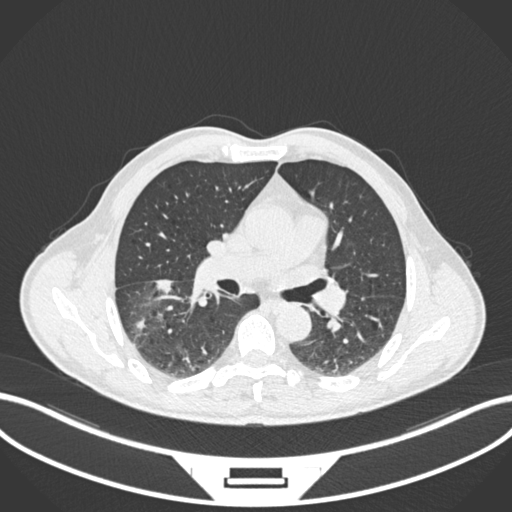
Chest CT, one axial slice; position 111 of 208 along the scan axis; 120 kVp; lung window (W 1500 / L -600 HU); 1 mm slice thickness; 512 × 512 image matrix, field of view 400 × 400 mm. Patient: male, 58 years. From the clinical record (not read from this slice): clinical TNM (as recorded): T3 N0 M0.
Outlined on this slice (rectangle marked by the reading radiologist):
- lung tumour (recorded histology: squamous cell carcinoma): bounding box [x1, y1, x2, y2] px = [150, 277, 180, 303]